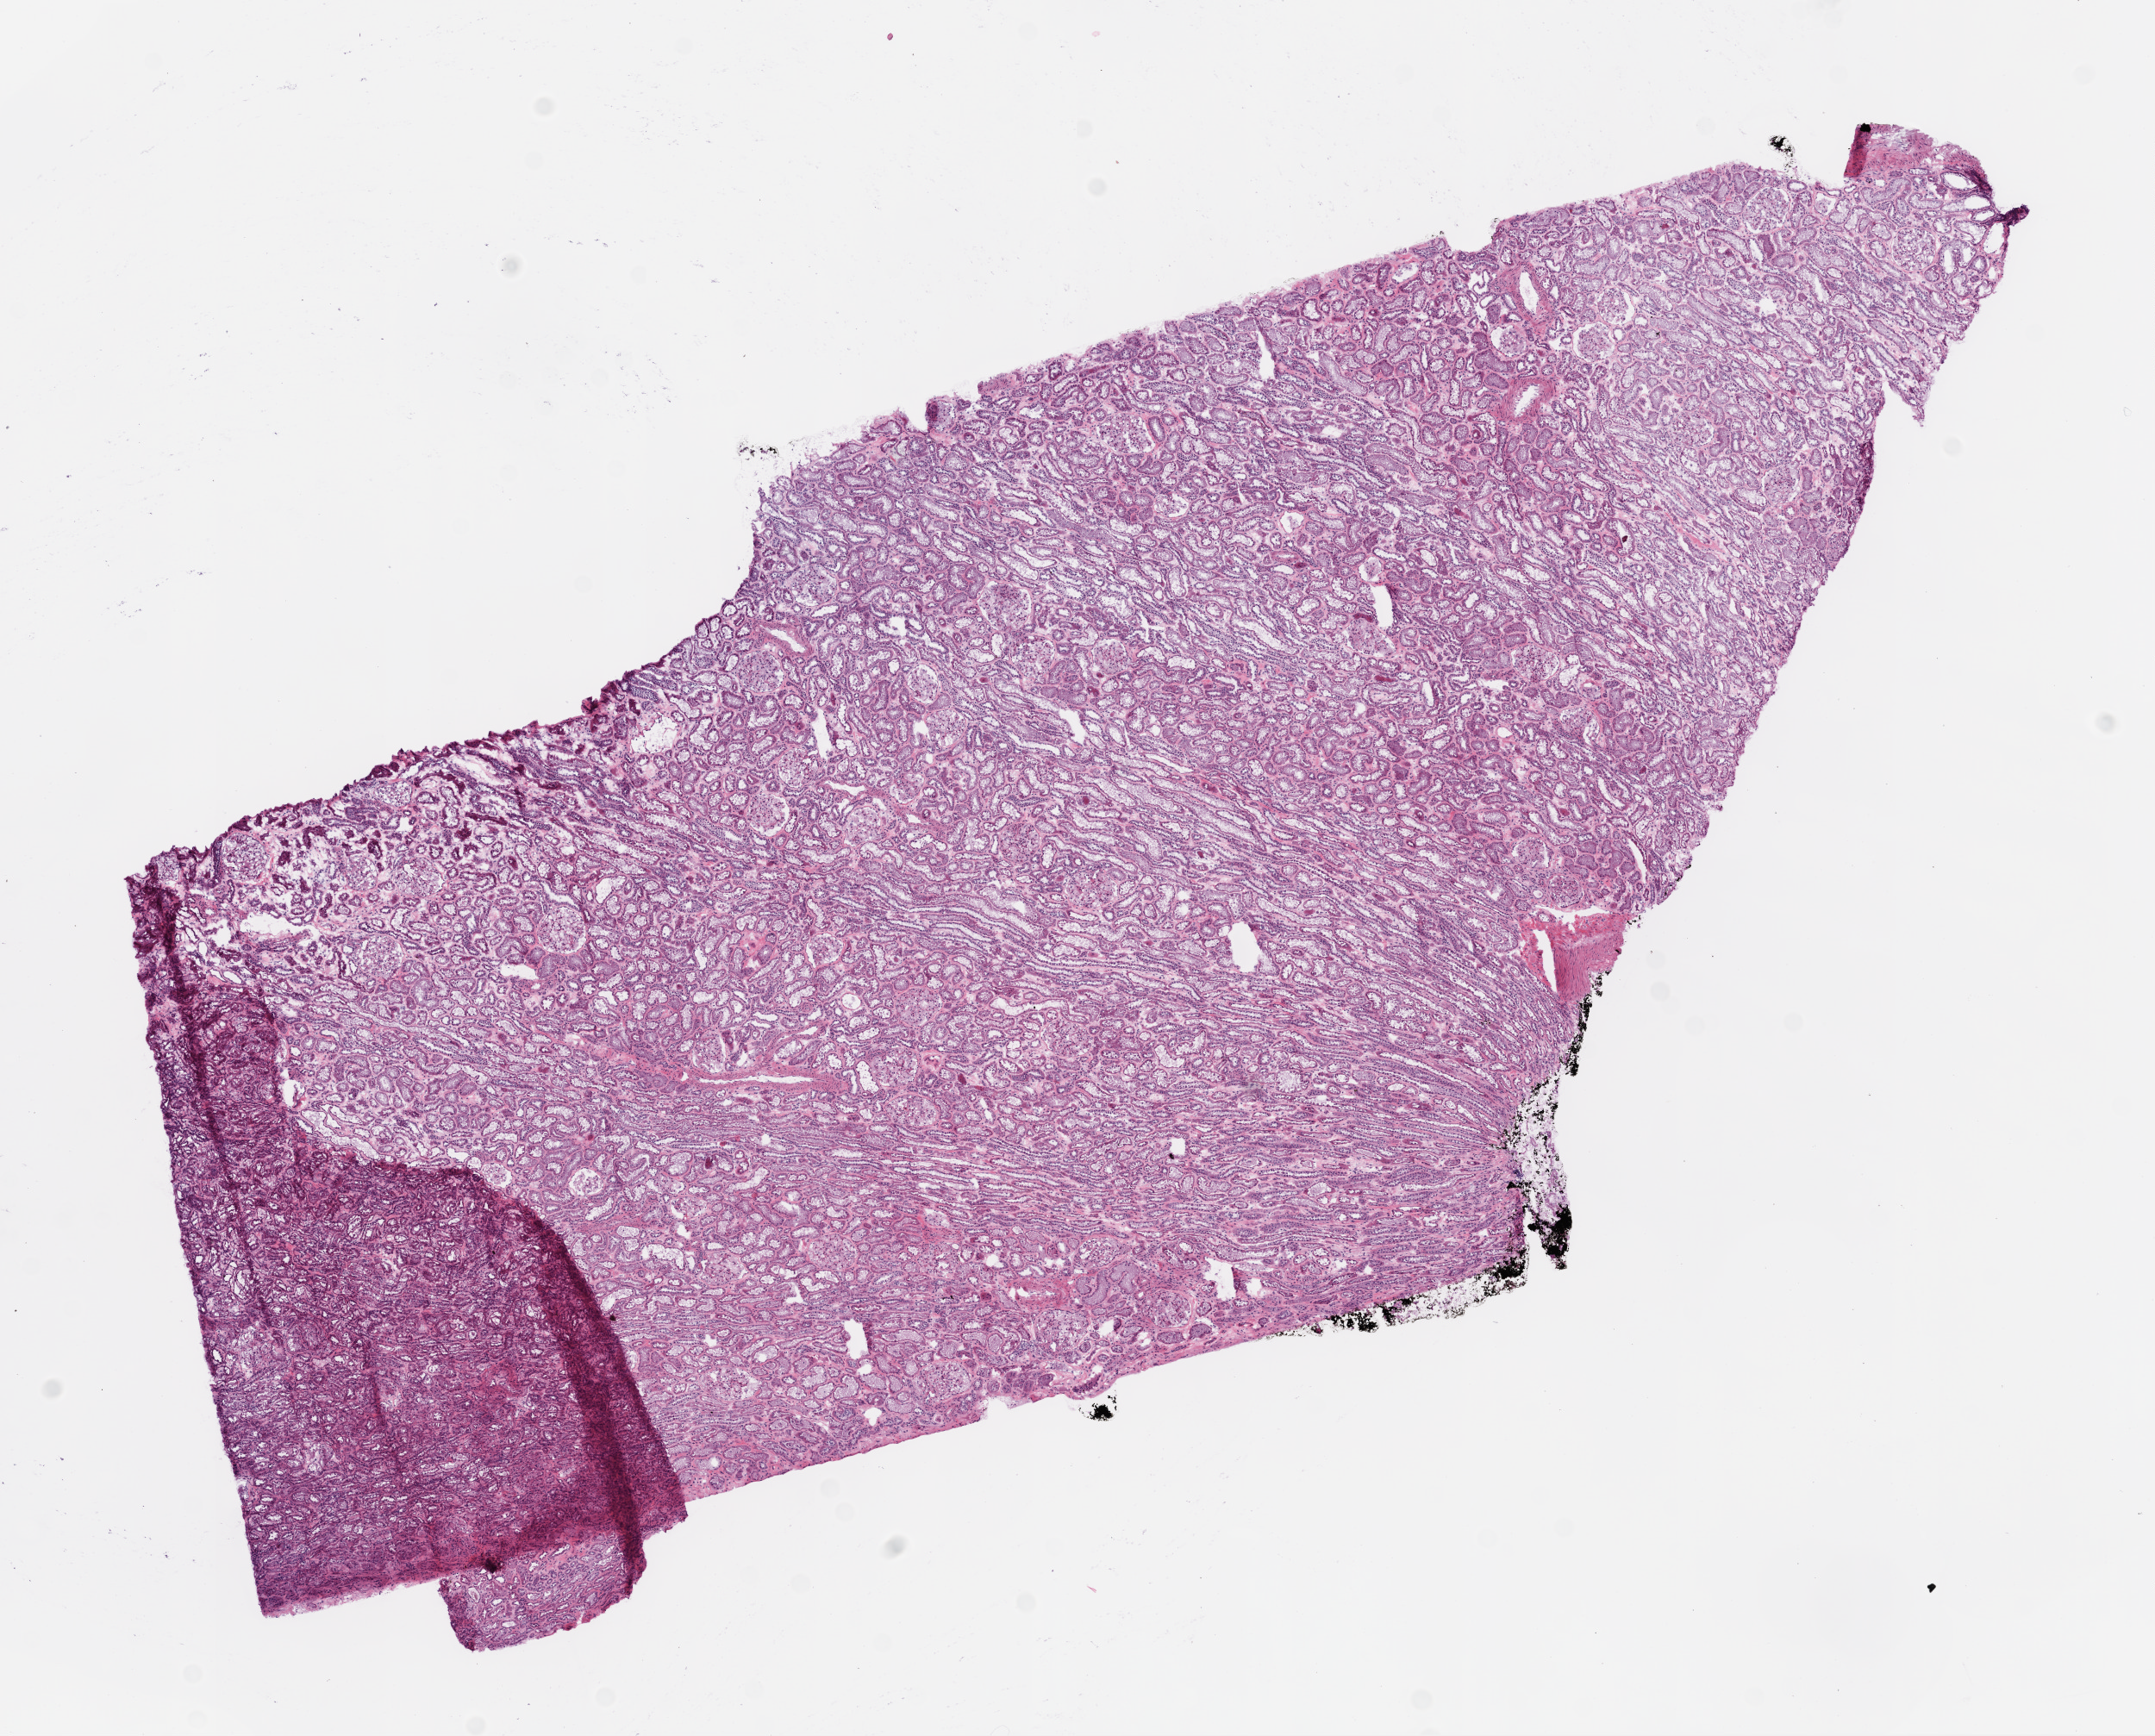
Whole-slide histology image, H&E, whole scanned area (about 10.0 x 8.1 mm, acquisition: 20x scan) shown as a low-resolution overview; frozen section from the top of the tissue portion; solid tissue normal (non-tumour tissue) sample from the kidney. Male, age 51 years at initial diagnosis.
* this section: solid tissue normal (non-tumour) sample from the same patient
* patient diagnosis: Clear cell adenocarcinoma, NOS